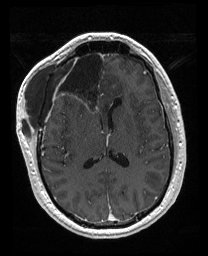
Brain MRI from a brain-tumour surgery series, one axial slice; position 84 of 176 along the scan axis; T1-weighted post-contrast; 1 mm slice thickness; 208 × 256 image matrix, field of view 208 × 256 mm. From the clinical record (not read from this slice): histopathology: Astrocytoma; WHO grade: 4; IDH mutation: yes.
Annotated regions visible in this slice (outlined manually by an expert reader):
- previous resection cavity: bounding box <56,52,106,111> (left, top, right, bottom; pixels)